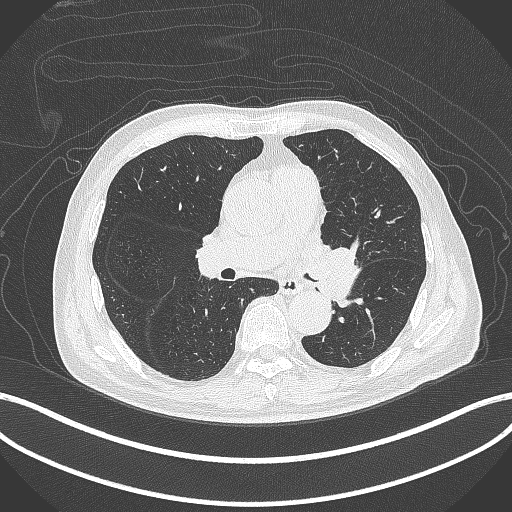
Chest CT, one axial slice; position 236 of 417 along the scan axis; 120 kVp; lung window (W 1500 / L -600 HU); 1 mm slice thickness; 512 × 512 image matrix. Male patient, age 77 years. Case-level facts recorded for this patient, not image findings: clinical TNM (as recorded): T3 N1 M0.
Outlined on this slice (rectangle marked by the reading radiologist):
- lung tumour (recorded histology: adenocarcinoma): box from (x=306, y=240) to (x=359, y=314) px